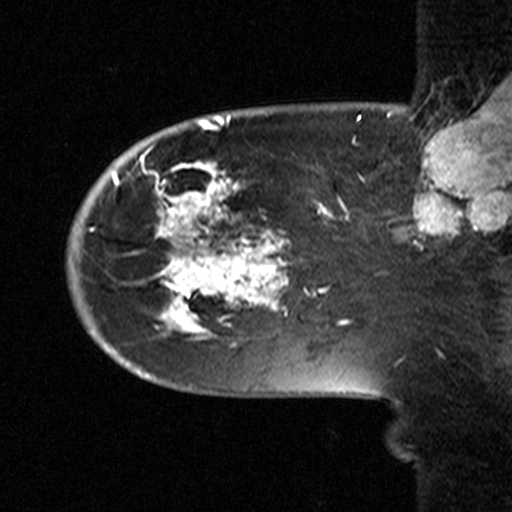
Breast MRI (dynamic contrast-enhanced), one sagittal slice; position 11 of 44 along the scan axis; dynamic contrast-enhanced study with each time point stored as its own series, time point 2 of 3 at this slice position (early post-contrast, ordered by acquisition time); 1.5 T; TE 4.5 ms, TR 11 ms; 512 × 512 image matrix, field of view 200 × 200 mm. Patient: female, 53 years. Case-level facts recorded for this patient, not image findings: setting: breast cancer imaged before/during neoadjuvant chemotherapy; receptor status: HR-positive, HER2-negative.
Outlined on this slice (semi-automatically segmented with operator editing):
- analysis volume of interest (the breast-tissue region the enhancement analysis was run in; not a lesion): bounding box <63,154,311,367> (left, top, right, bottom; pixels)
- tumour enhancement mask (voxels above the 90 % enhancement threshold inside the analysis volume of interest): <91,163,310,339>